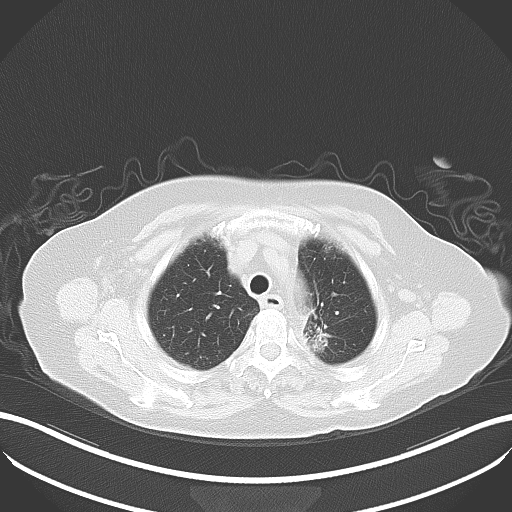
Chest CT, one axial slice; slice 33 of 42 in the series (ordered by position); reconstruction kernel B80f; lung window (W 1500 / L -600 HU); 6 mm slice thickness; 512 × 512 image matrix, field of view 400 × 400 mm. Patient: female, 81 years. From the clinical record (not read from this slice): clinical TNM (as recorded): T2a N0 M0.
Outlined on this slice (rectangle marked by the reading radiologist):
- lung tumour (recorded histology: adenocarcinoma): bounding box [x1, y1, x2, y2] px = [296, 318, 337, 364]